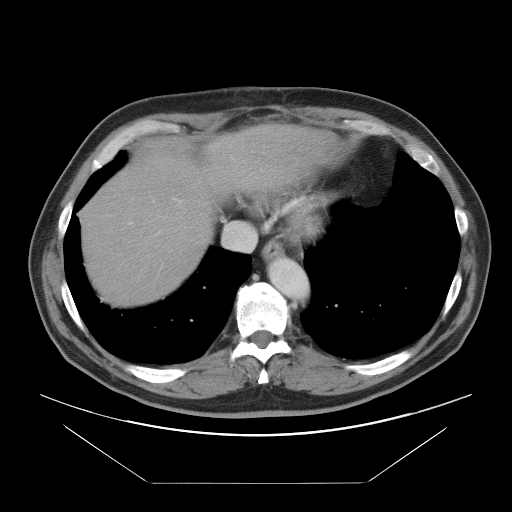
Contrast-enhanced abdominal CT, one axial slice; slice 82 of 97 in the series (ordered by position); intravenous contrast given; soft-tissue window (W 400 / L 40 HU); 5 mm slice thickness; 512 × 512 image matrix, field of view 442 × 442 mm. Male patient, age 62 years. Case-level facts recorded for this patient, not image findings: diagnosis: colorectal cancer liver metastases, imaged before liver resection; multiple liver metastases: no; largest metastasis: 7 cm; chemotherapy before resection: yes.
Structures marked on this image (expert manual segmentation):
- hepatic veins: bounding box (x1, y1, x2, y2) in pixels: (223, 222, 256, 251)
- liver: (82, 129, 320, 303)
- planned liver remnant (the part of the liver to remain after resection): (83, 179, 214, 303)
- portal vein (with intrahepatic branches): (130, 200, 180, 232)